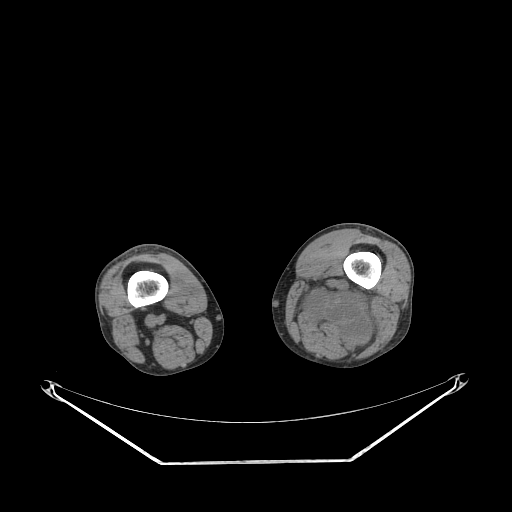
CT of an extremity soft-tissue mass (from a PET/CT study), one axial slice; slice 205 of 267 in the series (ordered by position); soft-tissue window (W 400 / L 40 HU); 512 × 512 image matrix, field of view 500 × 500 mm. Male patient. Case-level facts recorded for this patient, not image findings: histological type: undifferentiated pleomorphic liposarcoma; grade: high; site of the primary tumour: left thigh.
Structures marked on this image (expert contour drawn on MRI and transferred to this co-registered scan by the dataset authors):
- gross tumour volume including surrounding oedema: bounding box (x1, y1, x2, y2) in pixels: (294, 276, 375, 355)
- gross tumour volume (mass): (333, 315, 346, 325)